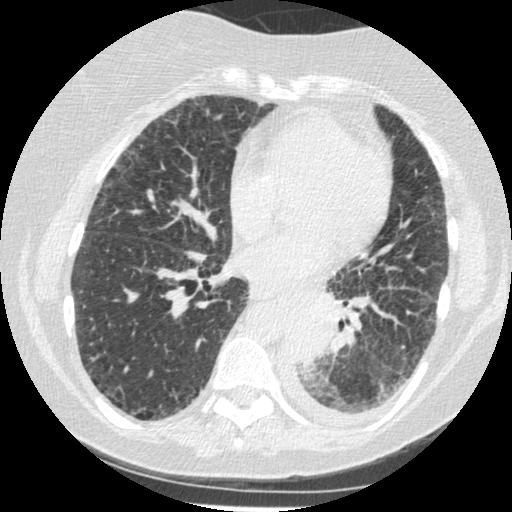
Axial slice from a low-dose chest CT screening exam; third annual screen; lung window (W 1500 / L -600 HU); 1.25 mm slice thickness; slice 246 of 341 in the series; 512 × 512 image matrix. Female, age 60 years at enrolment.
- Expert reader's lesion annotation, bounding box (x1, y1, x2, y2) in pixels: (277, 303, 343, 376).
- Screening reader's record for this exam (one nodule recorded; not confirmed to be the boxed lesion): non-calcified nodule or mass ≥4 mm, left lower lobe, 54 × 38 mm, smooth margins, soft tissue attenuation, pre-existing on the prior screen: yes; interval growth: yes.